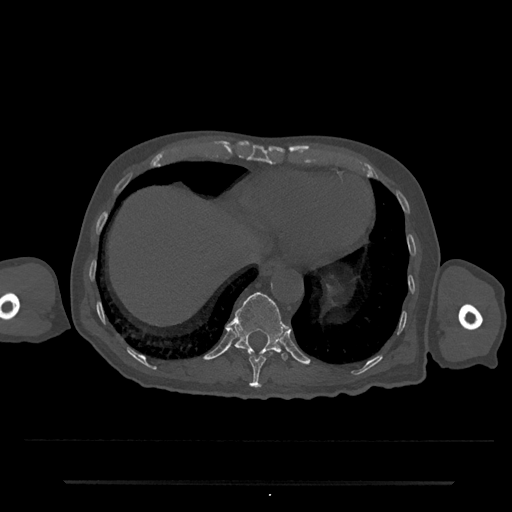
CT including the spine, one axial slice. Slice 279 of 797 in the series (ordered by position). 120 kVp. Bone window (W 1800 / L 400 HU). 0.5 mm slice thickness. 512 × 512 image matrix. Male patient, age 74 years. Case-level facts recorded for this patient, not image findings: primary cancer: prostate.
Structures marked on this image (semi-automatic segmentation, software-assisted and operator-edited):
- T10 vertebra: box from (x=247, y=350) to (x=275, y=388) px
- T11 vertebra: (x=227, y=292)–(x=288, y=361)